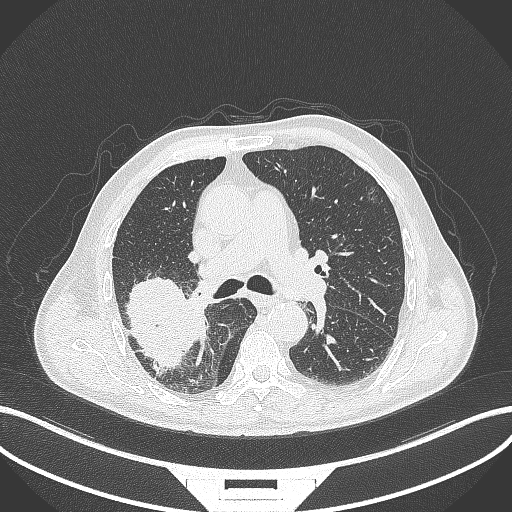
Chest CT, one axial slice; position 251 of 429 along the scan axis; lung window (W 1500 / L -600 HU); 1 mm slice thickness; 512 × 512 image matrix. Patient: male, 72 years. From the clinical record (not read from this slice): clinical TNM (as recorded): T3 N2 M0.
Annotated regions visible in this slice (rectangle marked by the reading radiologist):
- lung tumour (recorded histology: adenocarcinoma): bounding box <121,276,200,370> (left, top, right, bottom; pixels)